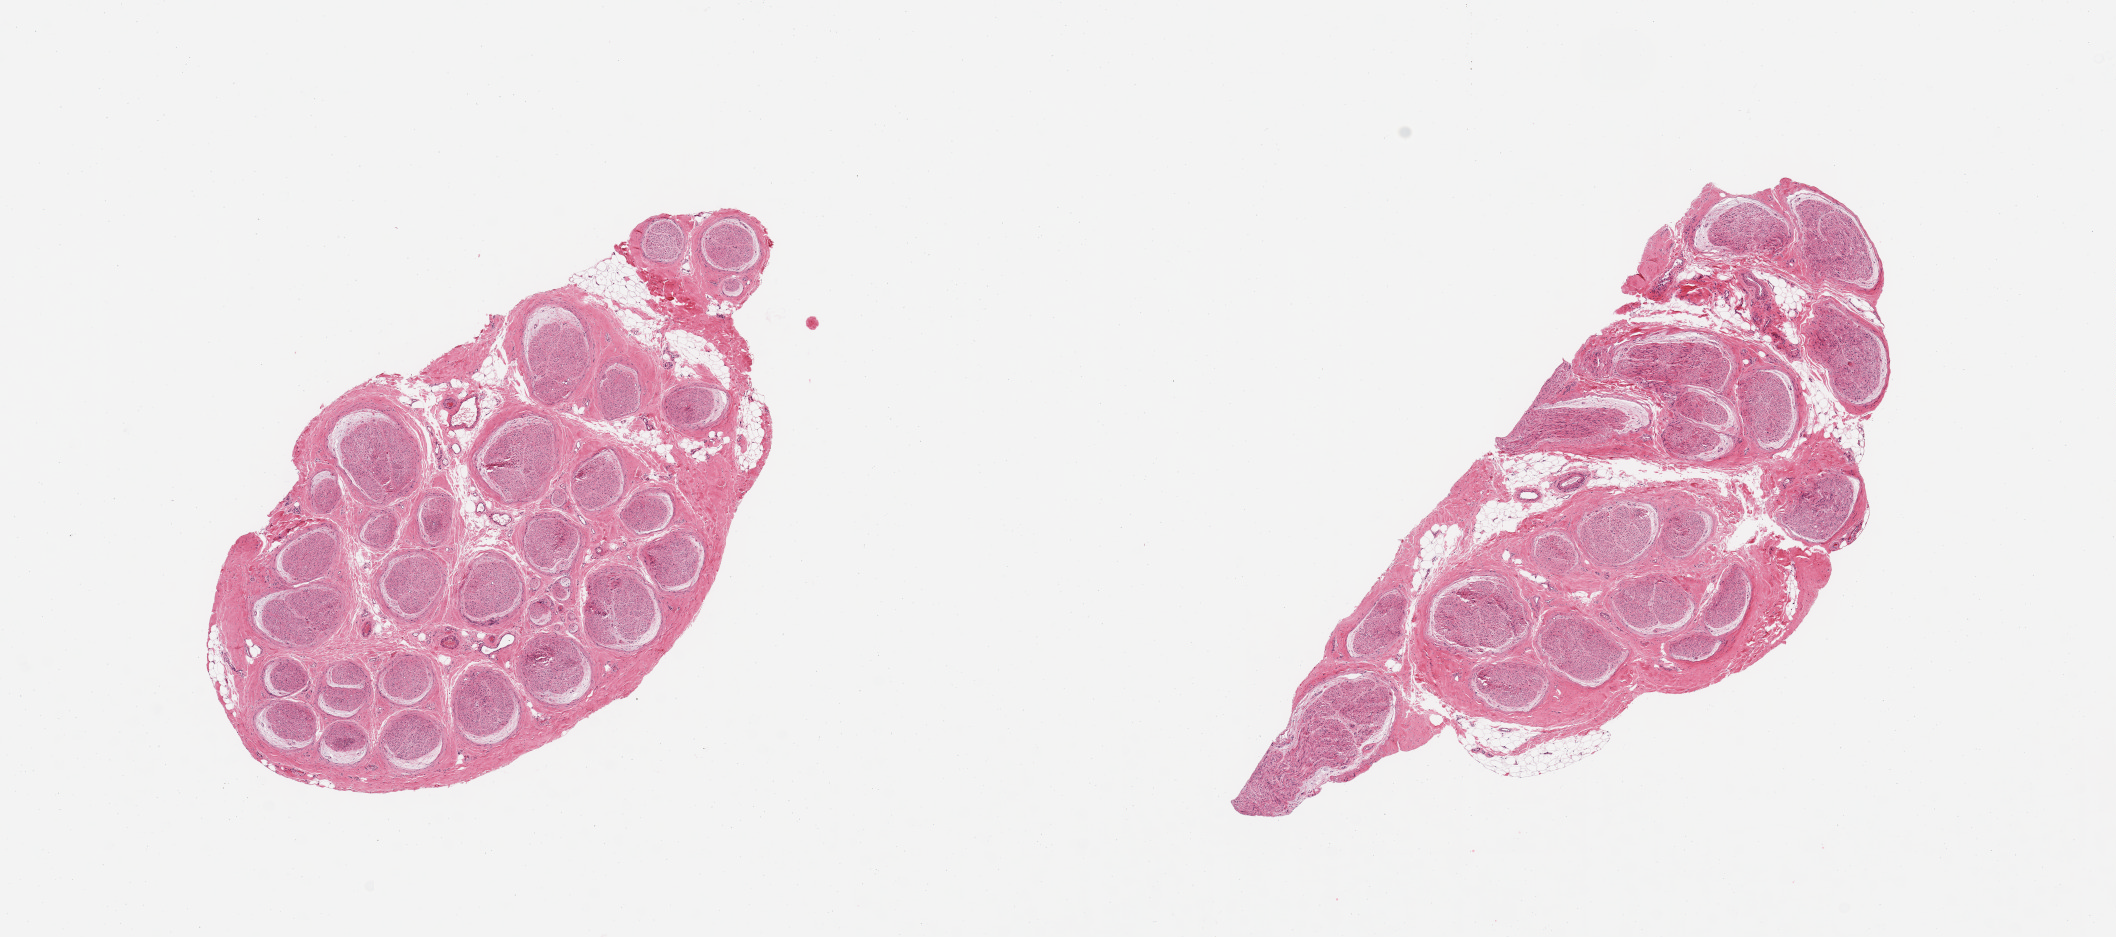
Hematoxylin and eosin (H&E) whole-slide image — whole scanned area (about 16.7 x 7.4 mm) shown as a low-resolution overview. PAXgene-fixed paraffin-embedded (PFPE) section. Section of tibial nerve (target tissue). Tissue donor sample. Male donor.
Reviewer comment on this tissue sample: 2 pieces, no adherent fat.